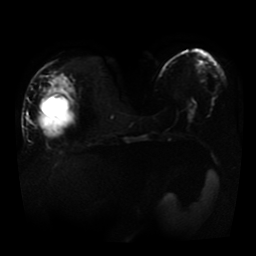
Breast MRI, one axial slice; position 13 of 41 along the scan axis; diffusion-weighted series; image 2 of 4 stored at this slice position (different b-values; order by instance number); 1.5 T; 5 mm slice thickness; 256 × 256 image matrix, field of view 360 × 360 mm. Female patient.
Structures marked on this image (expert manual segmentation):
- tumour on diffusion-weighted imaging: bounding box [x1, y1, x2, y2] px = [48, 78, 74, 96]